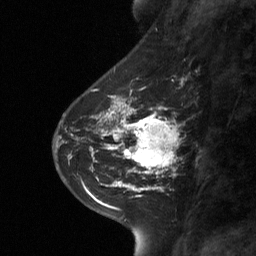
Breast MRI (dynamic contrast-enhanced), one sagittal slice. Slice 25 of 64 in the series (ordered by position). Dynamic contrast-enhanced study with each time point stored as its own series, time point 2 of 3 at this slice position (early post-contrast, ordered by acquisition time). 1.5 T. TE 4.8 ms, TR 27 ms. 2 mm slice thickness. 256 × 256 image matrix. Patient: female, 42 years. From the clinical record (not read from this slice): setting: breast cancer imaged before/during neoadjuvant chemotherapy; receptor status: triple-negative.
Outlined on this slice (semi-automatic segmentation, software-assisted and operator-edited):
- analysis volume of interest (the breast-tissue region the enhancement analysis was run in; not a lesion): box from (x=111, y=104) to (x=178, y=178) px
- tumour enhancement mask (voxels above the 90 % enhancement threshold inside the analysis volume of interest): (x=111, y=104)–(x=176, y=174)